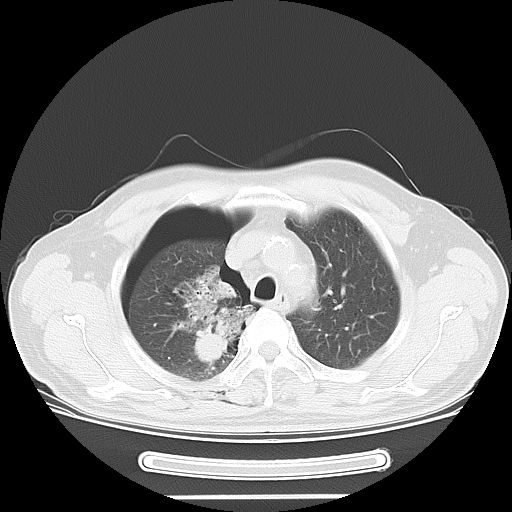
Chest CT, one axial slice. Slice 45 of 57 in the series (ordered by position). 120 kVp. Lung window (W 1500 / L -600 HU). 5 mm slice thickness. 512 × 512 image matrix, field of view 376 × 376 mm. Patient: male, 61 years. From the clinical record (not read from this slice): clinical TNM (as recorded): T1c N3 M1b.
Annotated regions visible in this slice (rectangle marked by the reading radiologist):
- lung tumour (recorded histology: adenocarcinoma): bounding box [x1, y1, x2, y2] px = [167, 267, 257, 367]